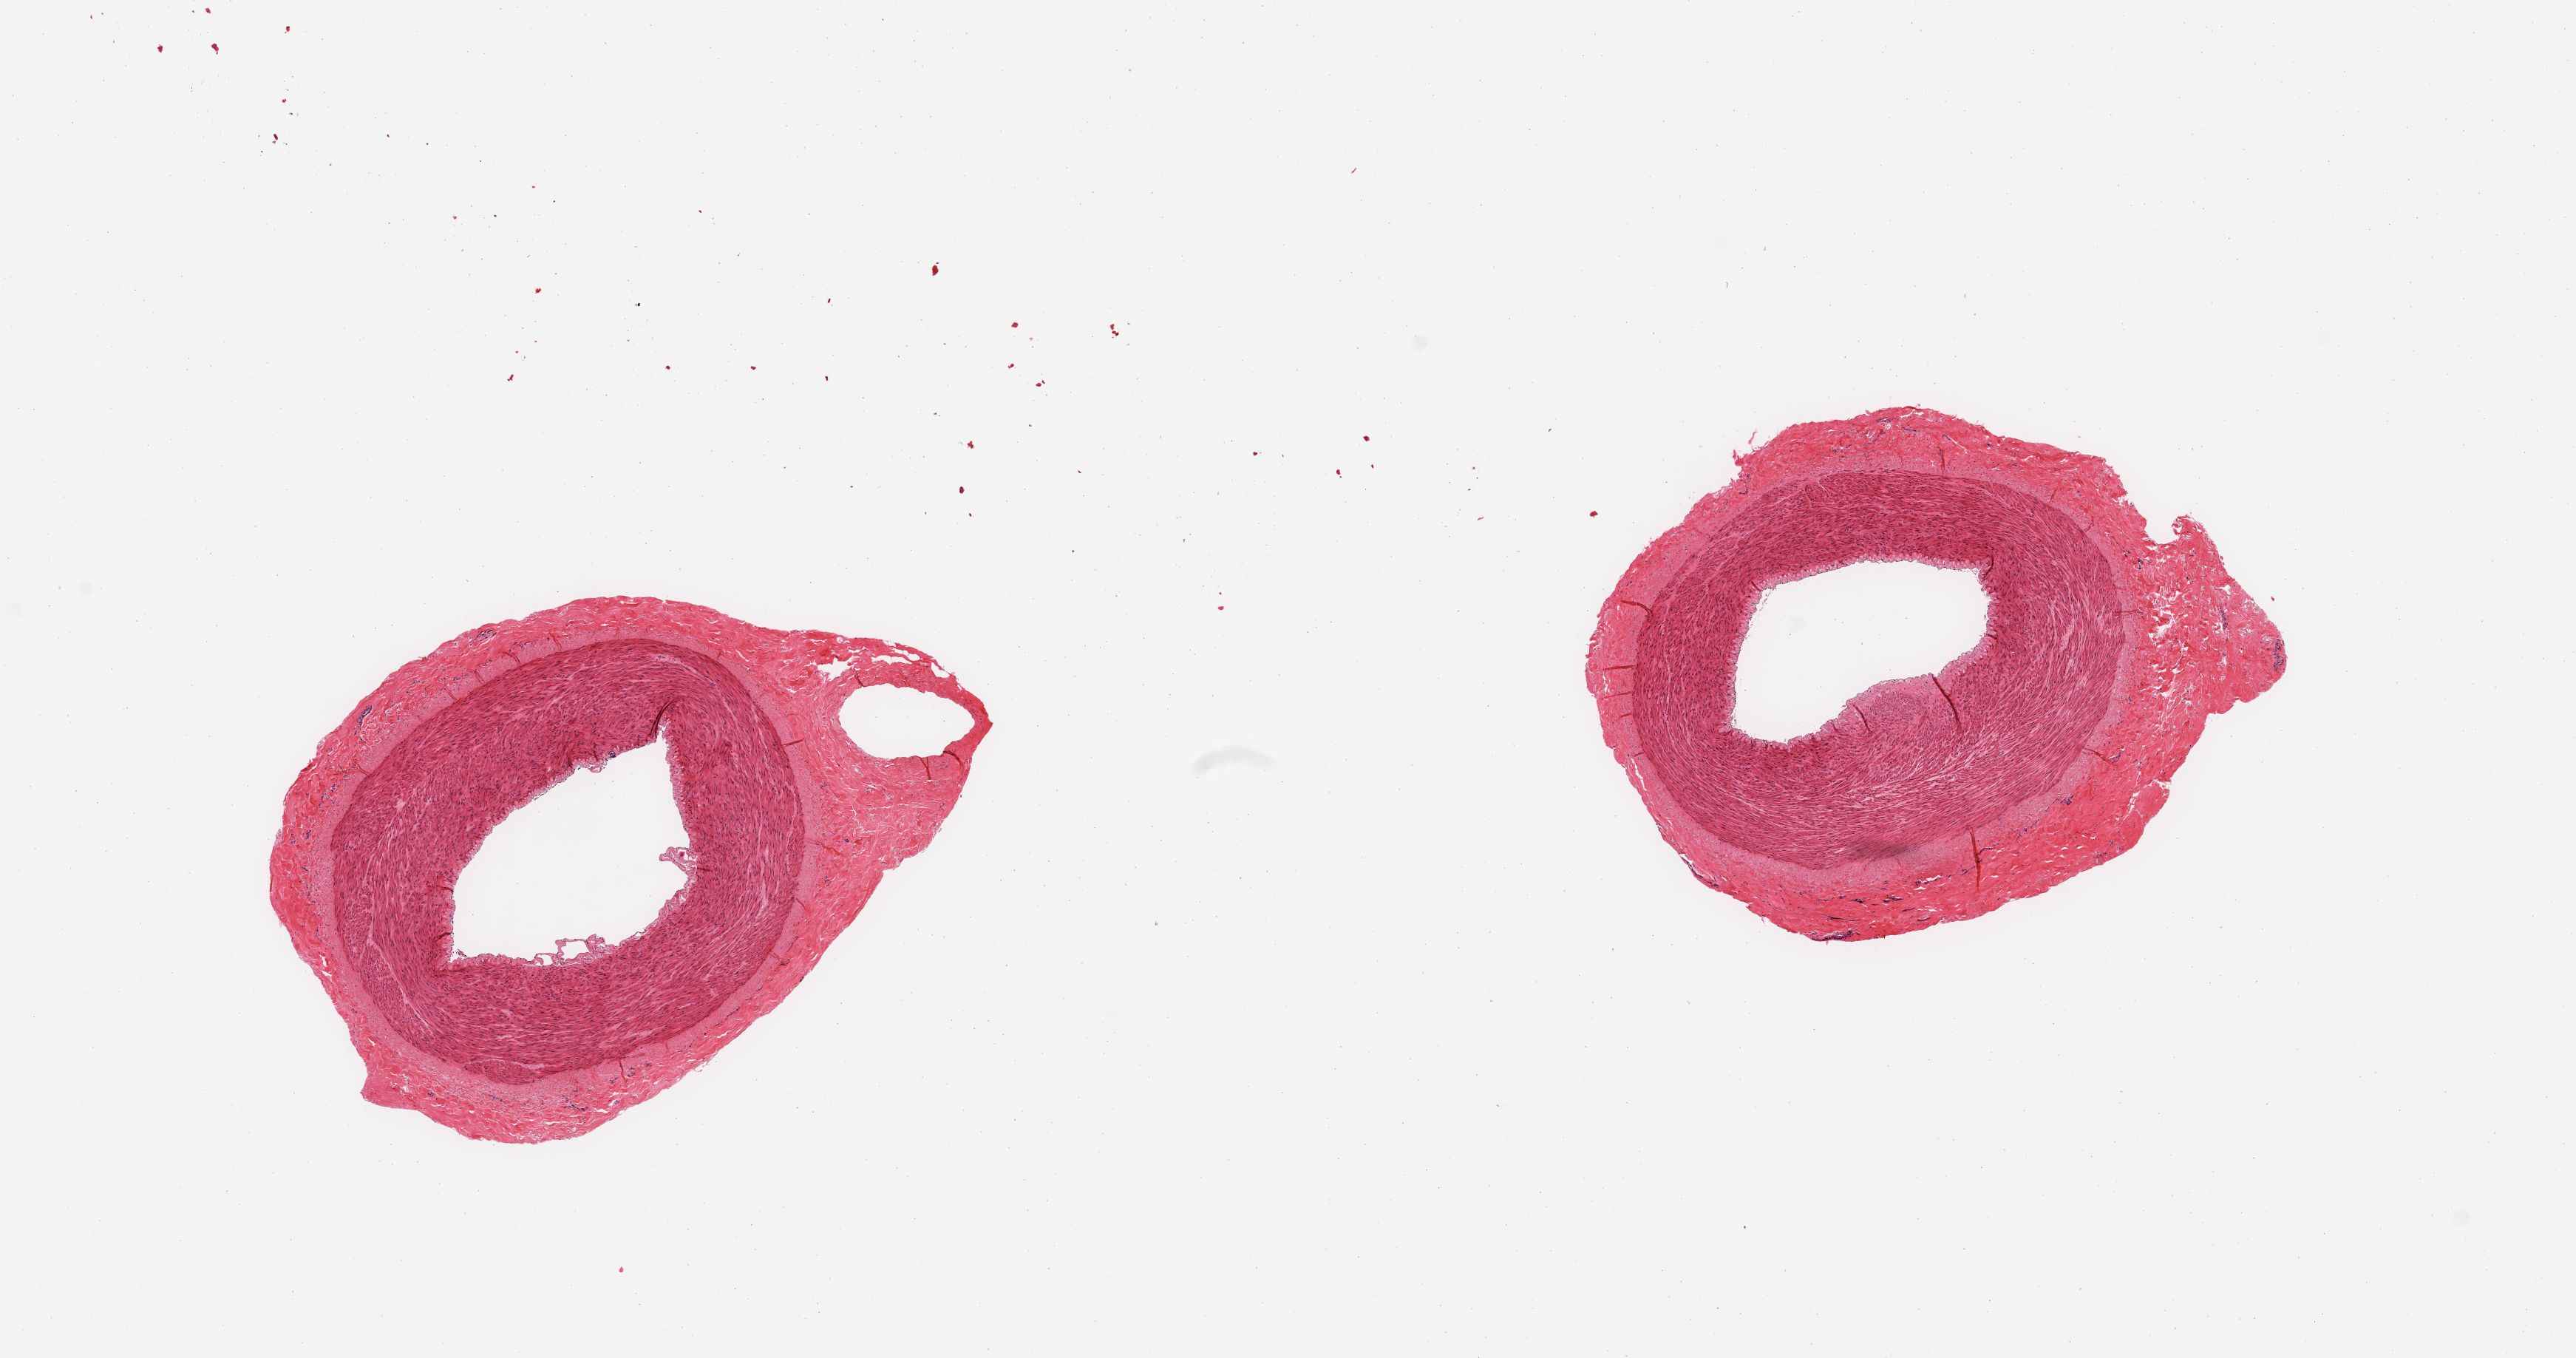
Haematoxylin and eosin whole-slide image, shown as a low-resolution overview of the whole scanned area (about 13.8 x 7.3 mm, acquisition: 20x scan), PAXgene-fixed, paraffin-embedded tissue, sampled site (target tissue): tibial artery, tissue donor sample. Male donor.
Pathologist's review note for this sample: 2 pieces, rim of fibrous tissue, ~0.5-1mm, both sections.